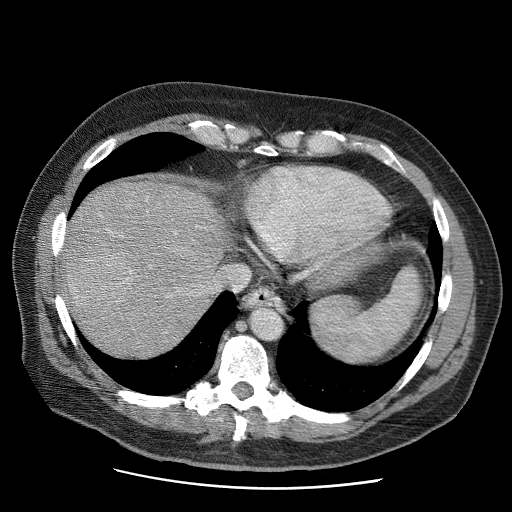
Contrast-enhanced abdominal CT (liver protocol), one axial slice; slice 53 of 81 in the series (ordered by position); 120 kVp; soft-tissue window (W 400 / L 40 HU); 2.5 mm slice thickness; 512 × 512 image matrix. From the clinical record (not read from this slice): diagnosis: hepatocellular carcinoma (patient treated with transarterial chemoembolisation; whether this scan precedes or follows treatment is not stated here); TNM stage (as recorded): Stage-IIIA; Child-Pugh class: A; tumour differentiation: moderately differentiated; tumour nodularity: multinodular.
Structures marked on this image (semi-automatic segmentation, software-assisted and operator-edited):
- liver parenchyma outside the tumour (the mass and vessels are separate outlines, so this box may not span the whole liver): bounding box <60,180,228,356> (left, top, right, bottom; pixels)
- mass: <58,232,140,319>